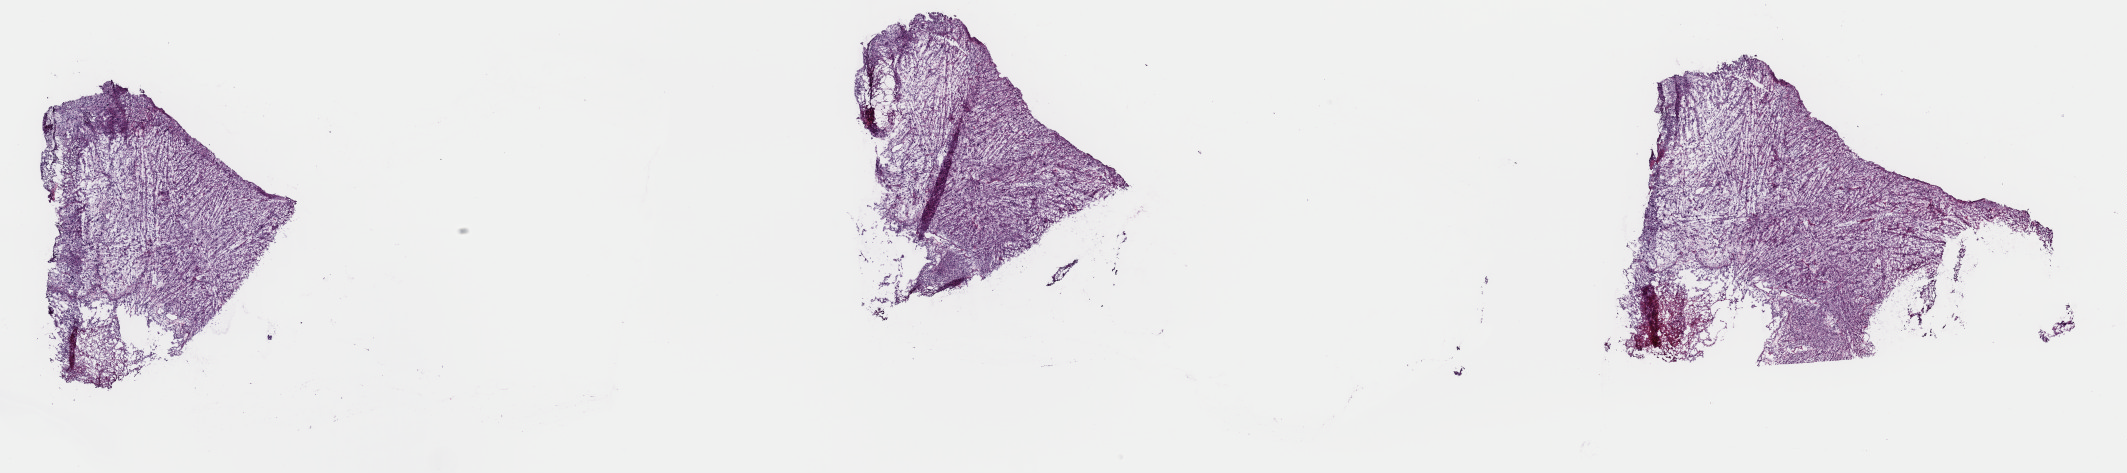
Whole-slide histology image, H&E-stained — a low-resolution overview of the entire scanned area, about 33.6 x 7.5 mm (from a 40x scan). Frozen section from the top of the tissue portion. Primary tumour sample from the retroperitoneum and peritoneum. Patient: male, age at initial diagnosis 66 years. Composition of this section per pathologist review: tumour cells 100%, tumour nuclei 88%, normal cells 0%, stromal cells 0%, necrosis 0%. Inflammatory infiltration, as recorded: lymphocyte infiltration 0%, monocyte infiltration 0%, neutrophil infiltration 0%.
• pathologic diagnosis: Dedifferentiated liposarcoma (retroperitoneum)